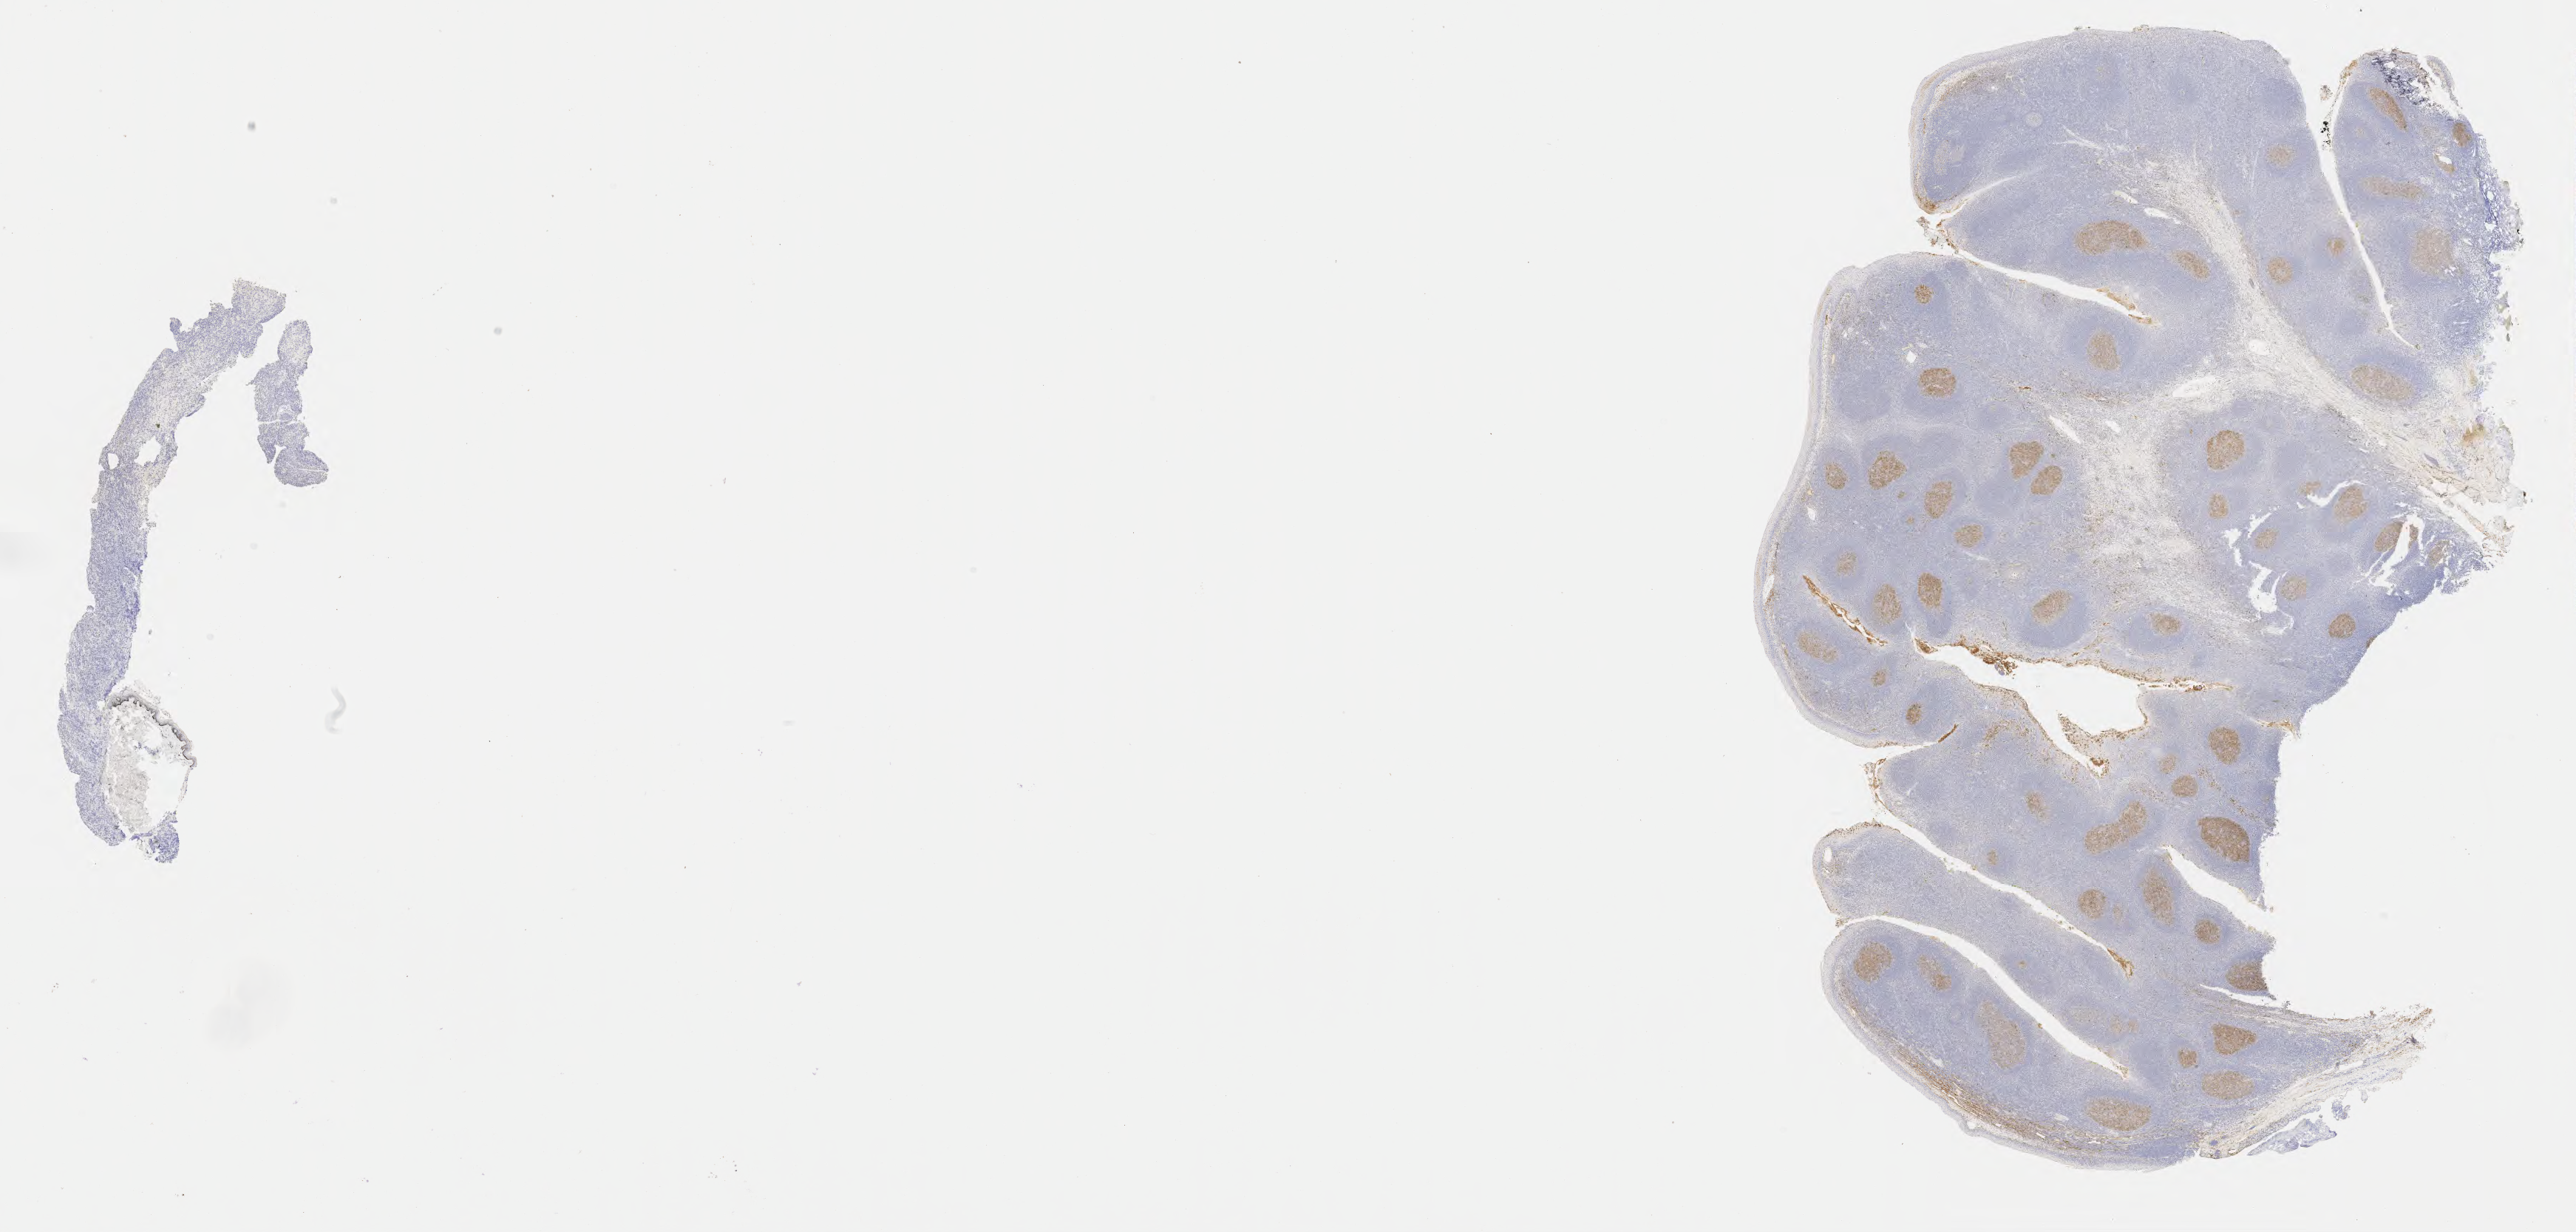
Immunohistochemistry (IHC) whole-slide image stained for CD10, a low-resolution overview of the entire scanned area, about 28.2 x 13.5 mm, specimen: tumor tissue. Female patient, age 43 years.
Diagnosis: Diffuse large B-cell lymphoma, NOS.